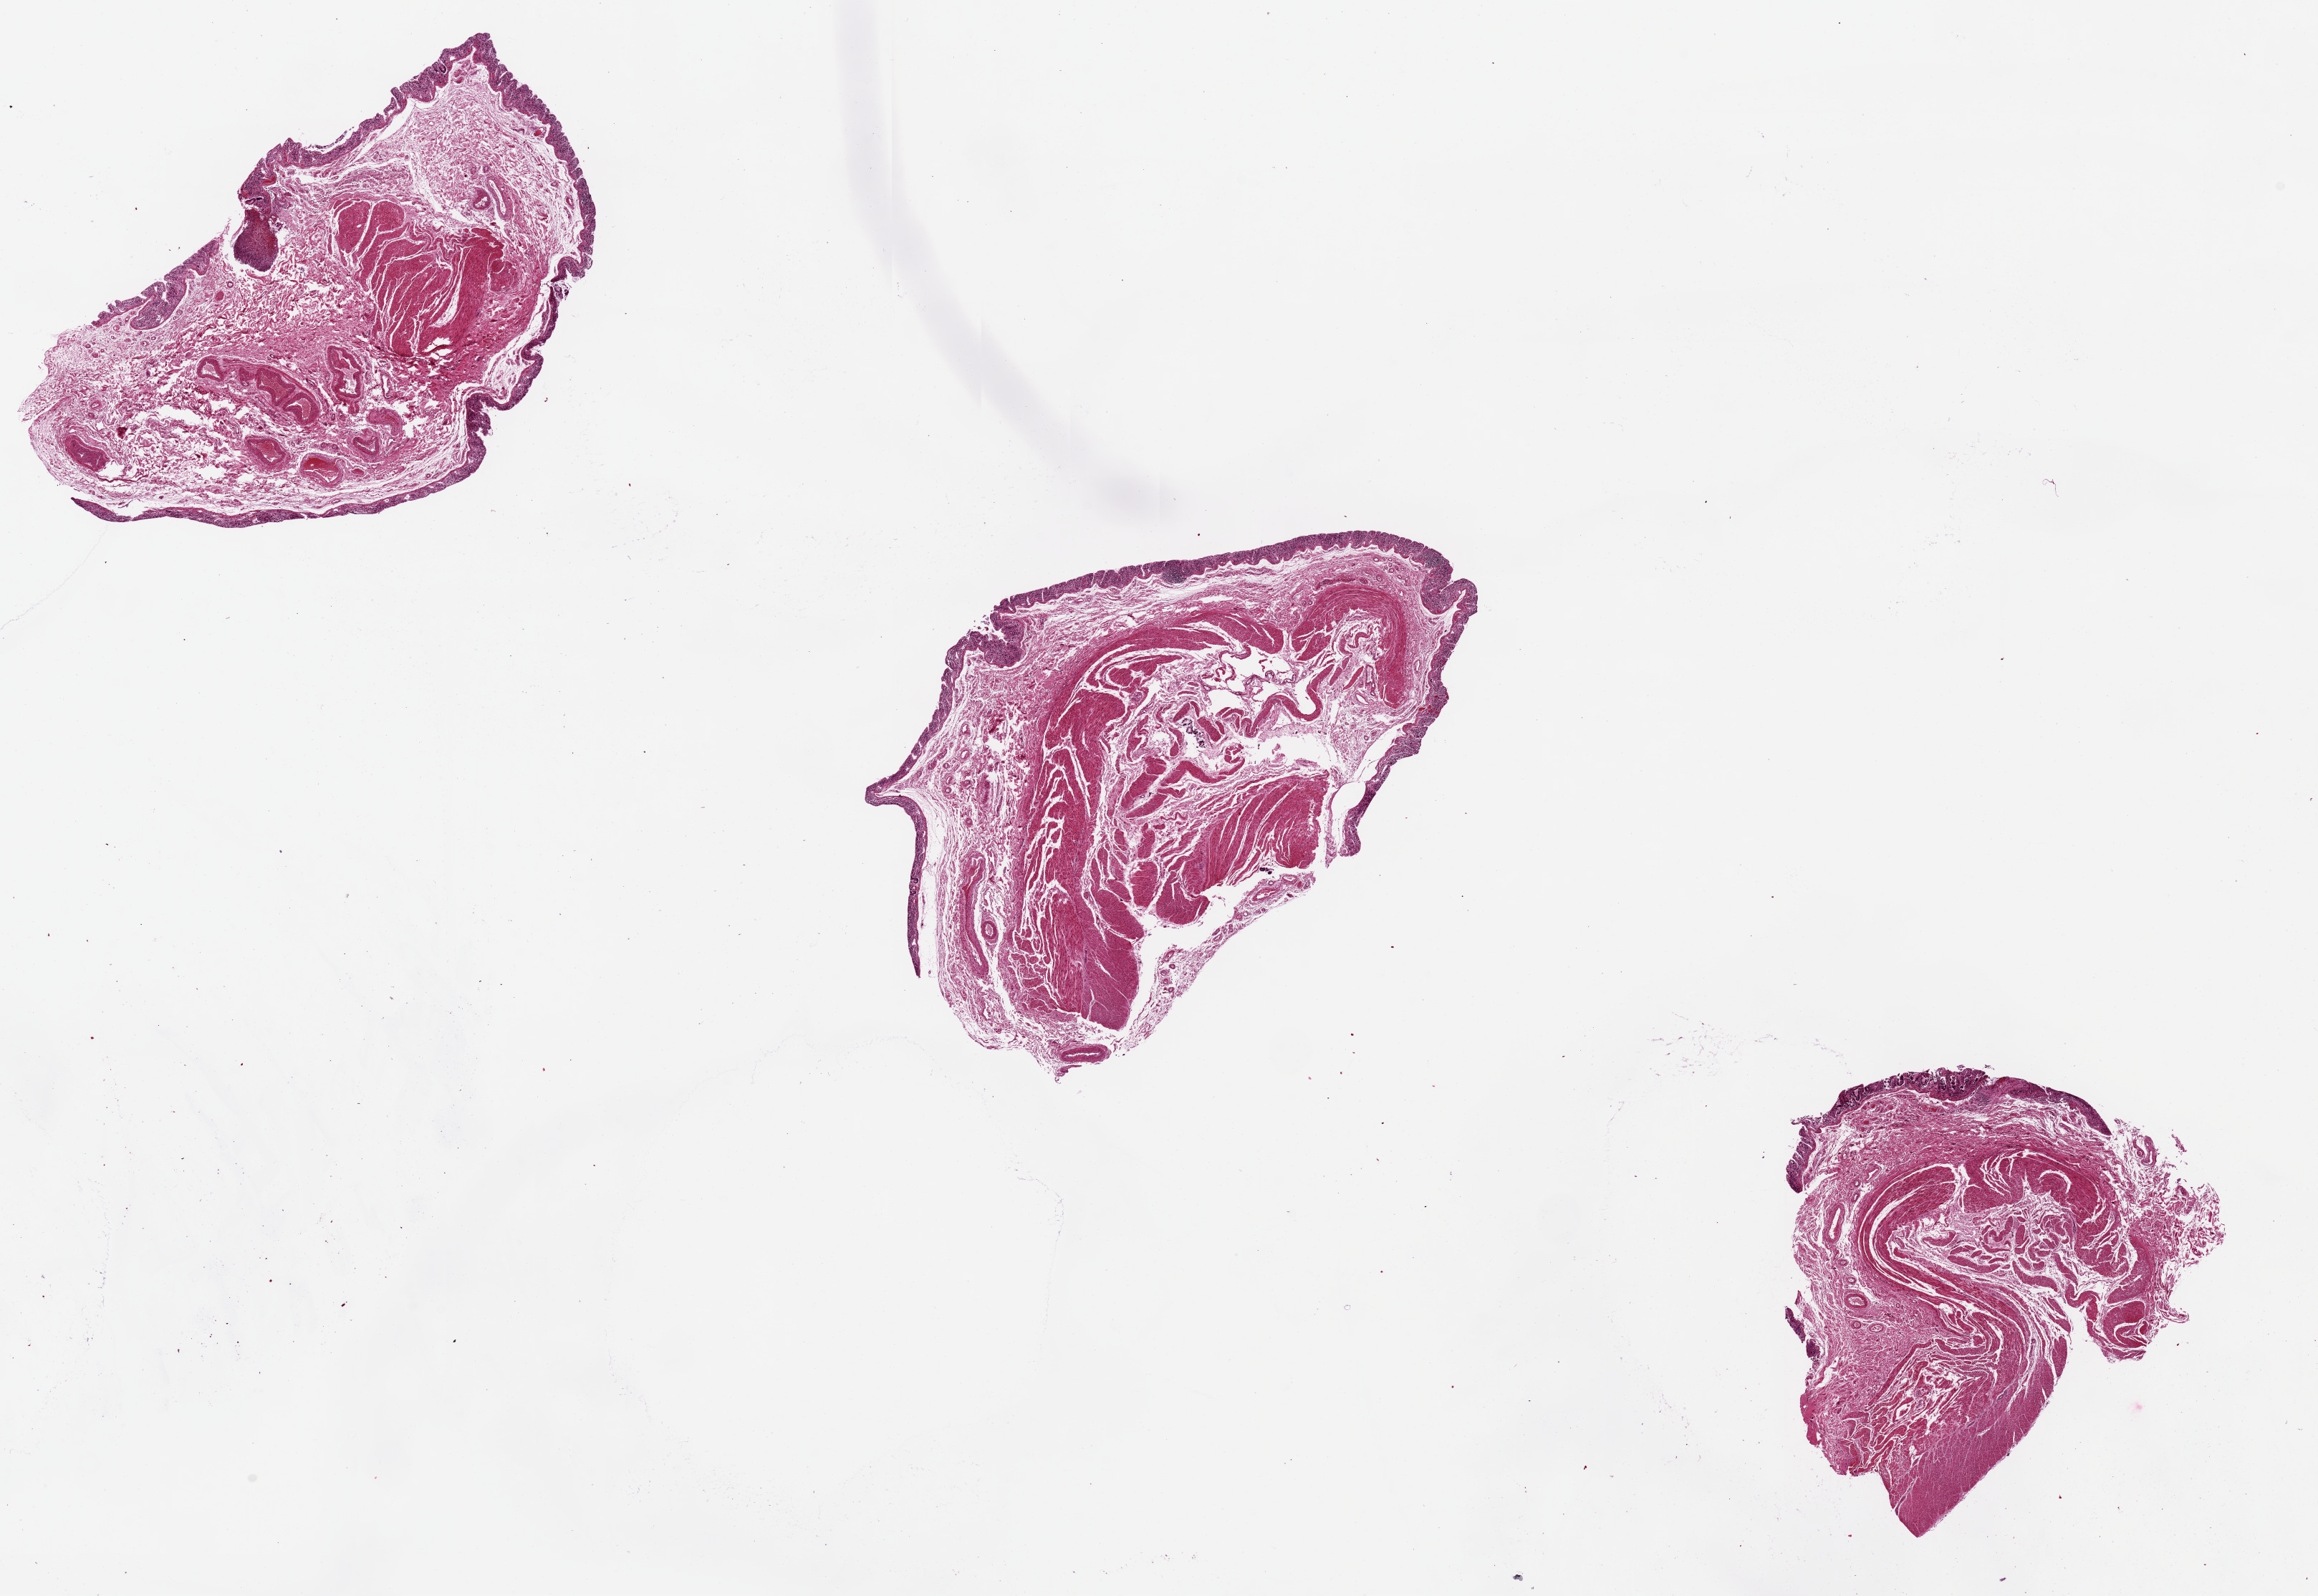
Digitized hematoxylin and eosin (H&E)-stained section — a low-resolution overview of the entire scanned area, about 25.6 x 17.6 mm; PAXgene-fixed paraffin-embedded (PFPE) section; sampled site (target tissue): transverse colon; tissue donor sample. Donor: female.
Pathologist's review note for this sample: 3 total glandular autolysis.